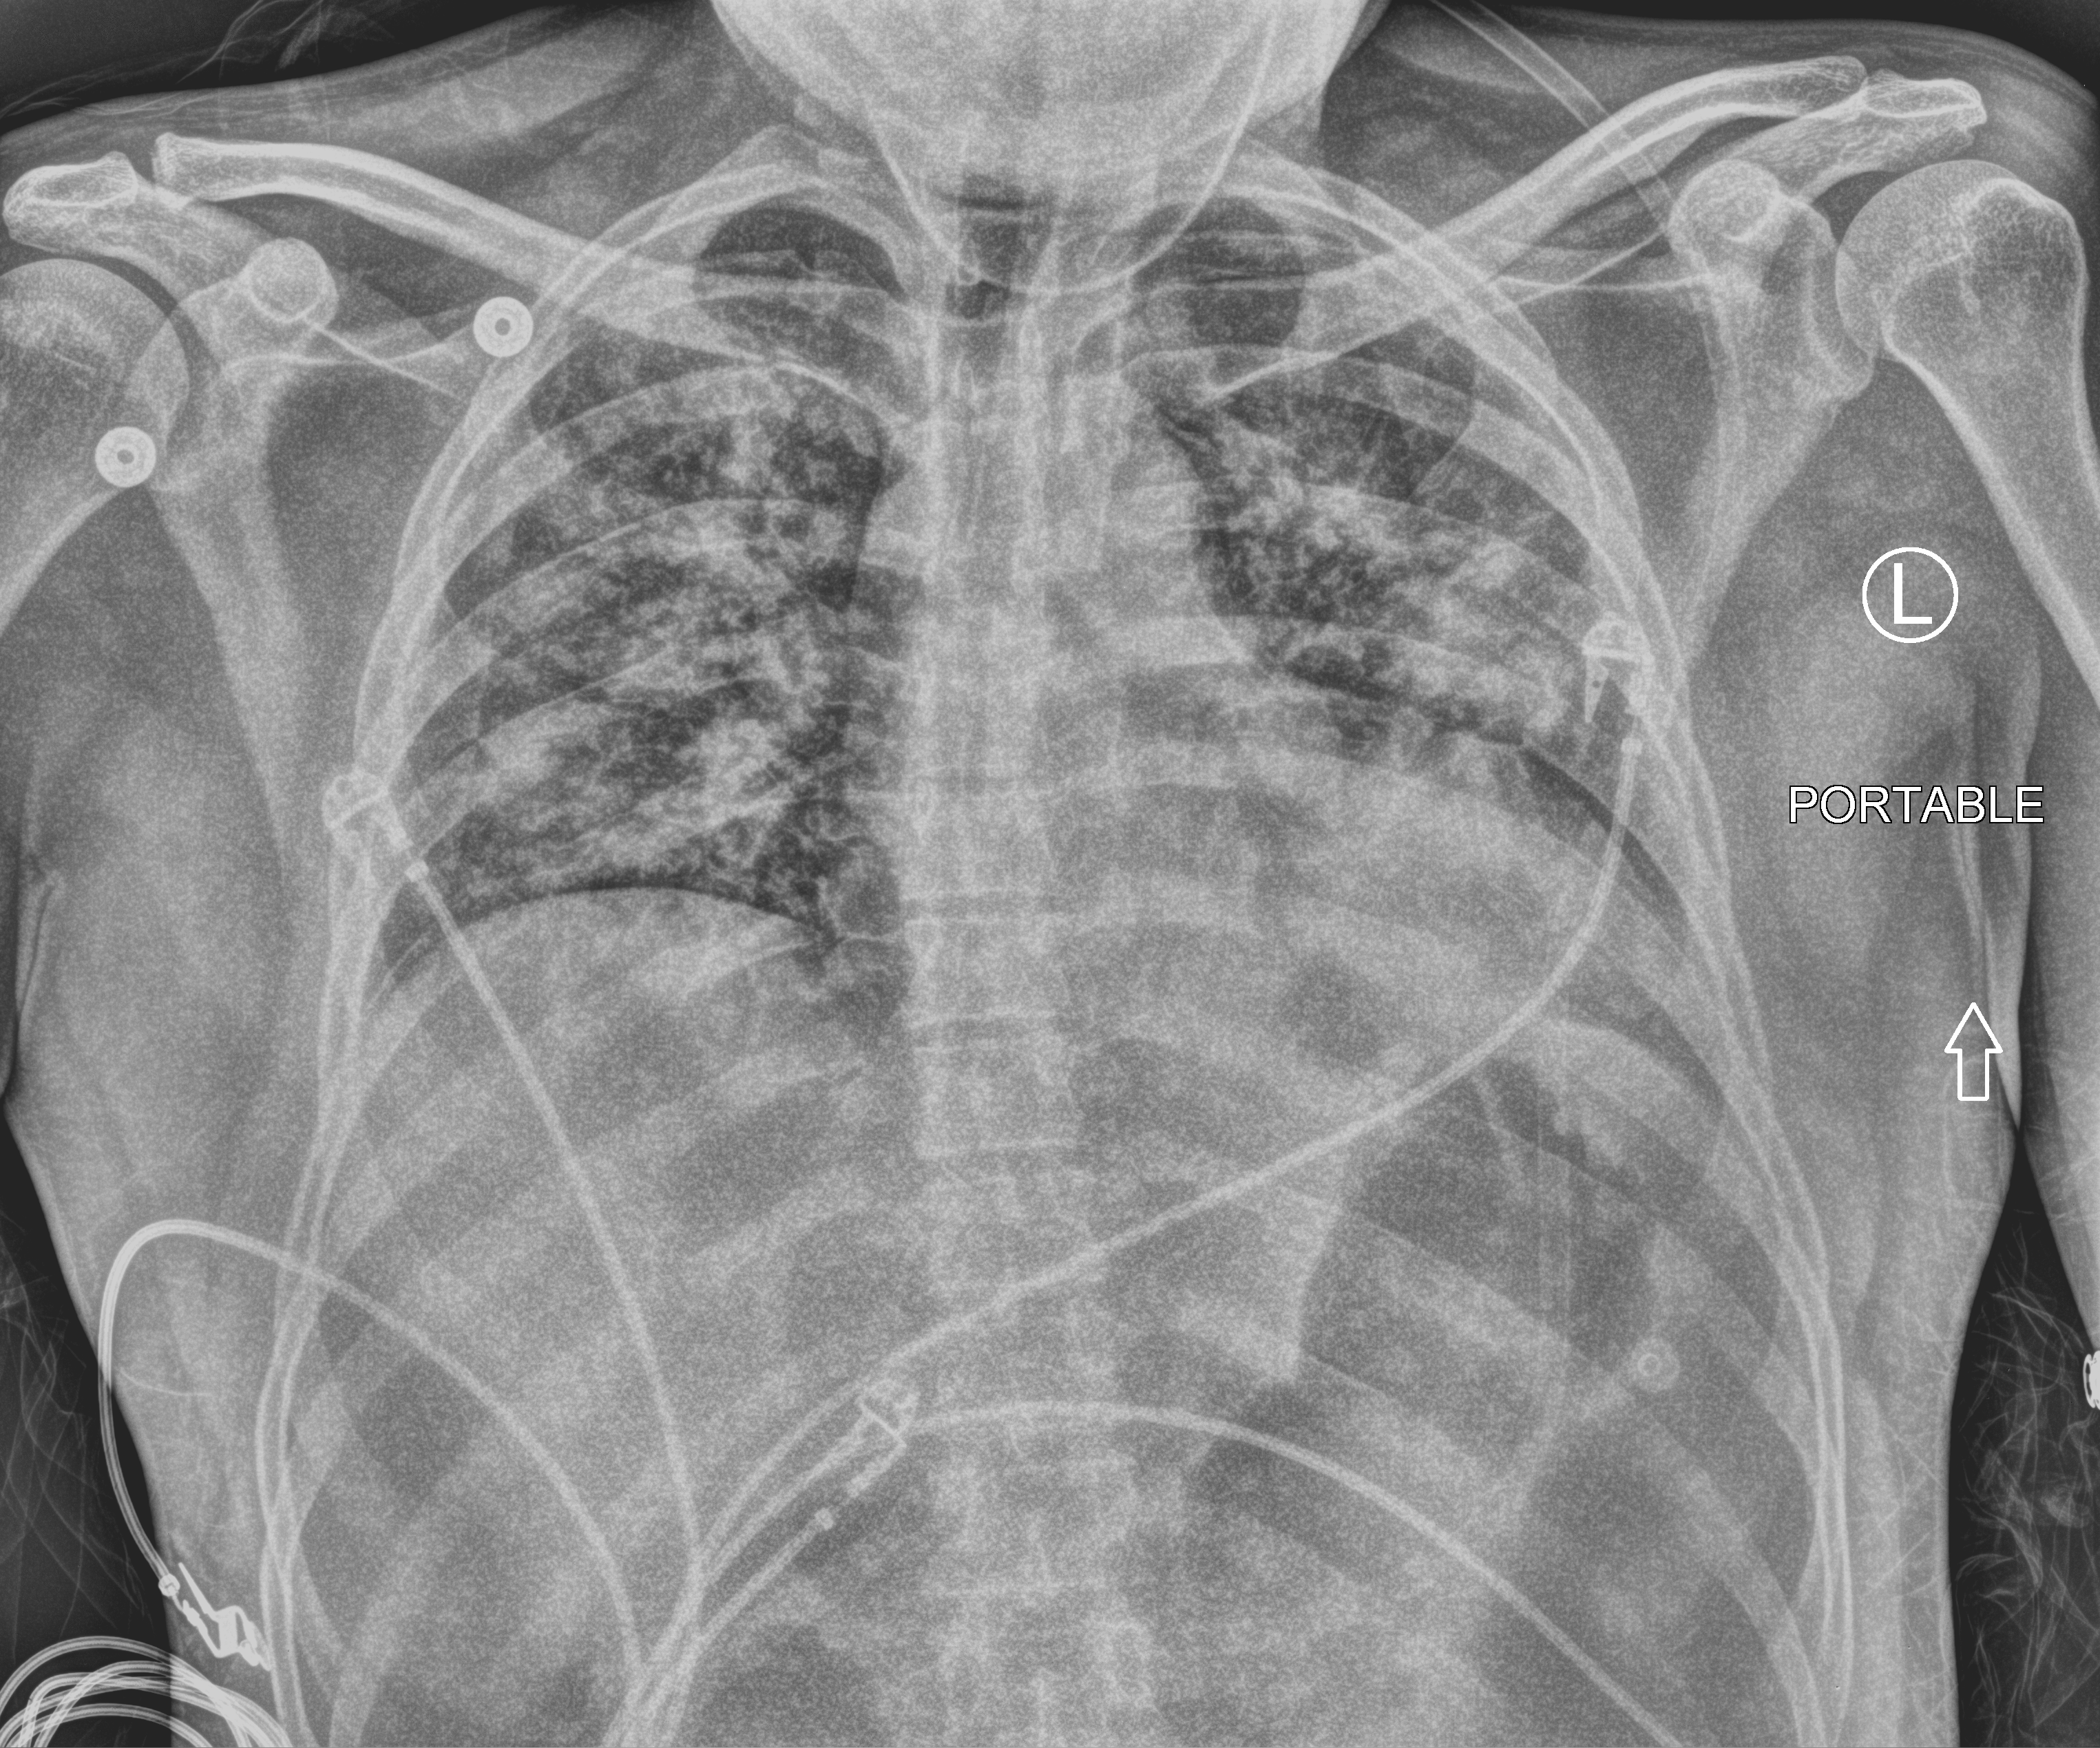
Portable chest radiograph, anteroposterior (AP) projection. Patient hospitalised with COVID-19; male, aged 18–59 years.
Hospital-stay facts (about this admission, not read from this image; timing relative to this image not recorded): chronic kidney disease (admission record): no.